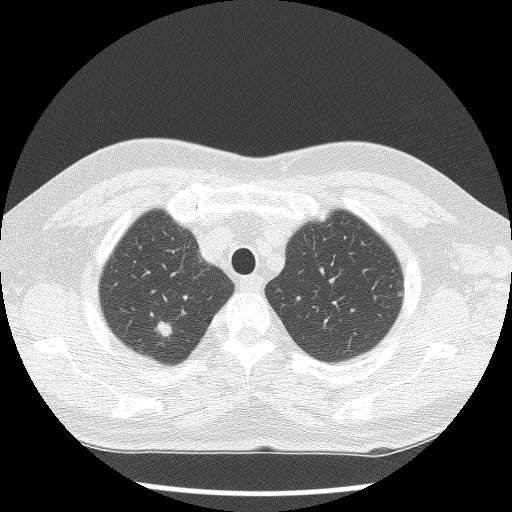
Axial slice from a low-dose chest CT screening exam, first (baseline) screen, lung window (W 1500 / L -600 HU), lung (sharp) reconstruction kernel (BONE). Male, age 70 years at enrolment. Current smoker at enrolment.
Expert reader's lesion annotation, bounding box <131,311,189,356> (left, top, right, bottom; pixels). Screening reader's record for this exam (one nodule recorded; not confirmed to be the boxed lesion): non-calcified nodule or mass ≥4 mm, right upper lobe, 12 × 10 mm, smooth margins, soft tissue attenuation. Later outcome: lung cancer diagnosed 14 days after this screen — large cell neuroendocrine carcinoma, right upper lobe, poorly differentiated (G3), stage IA (AJCC 6th edition), 15 mm at pathology.